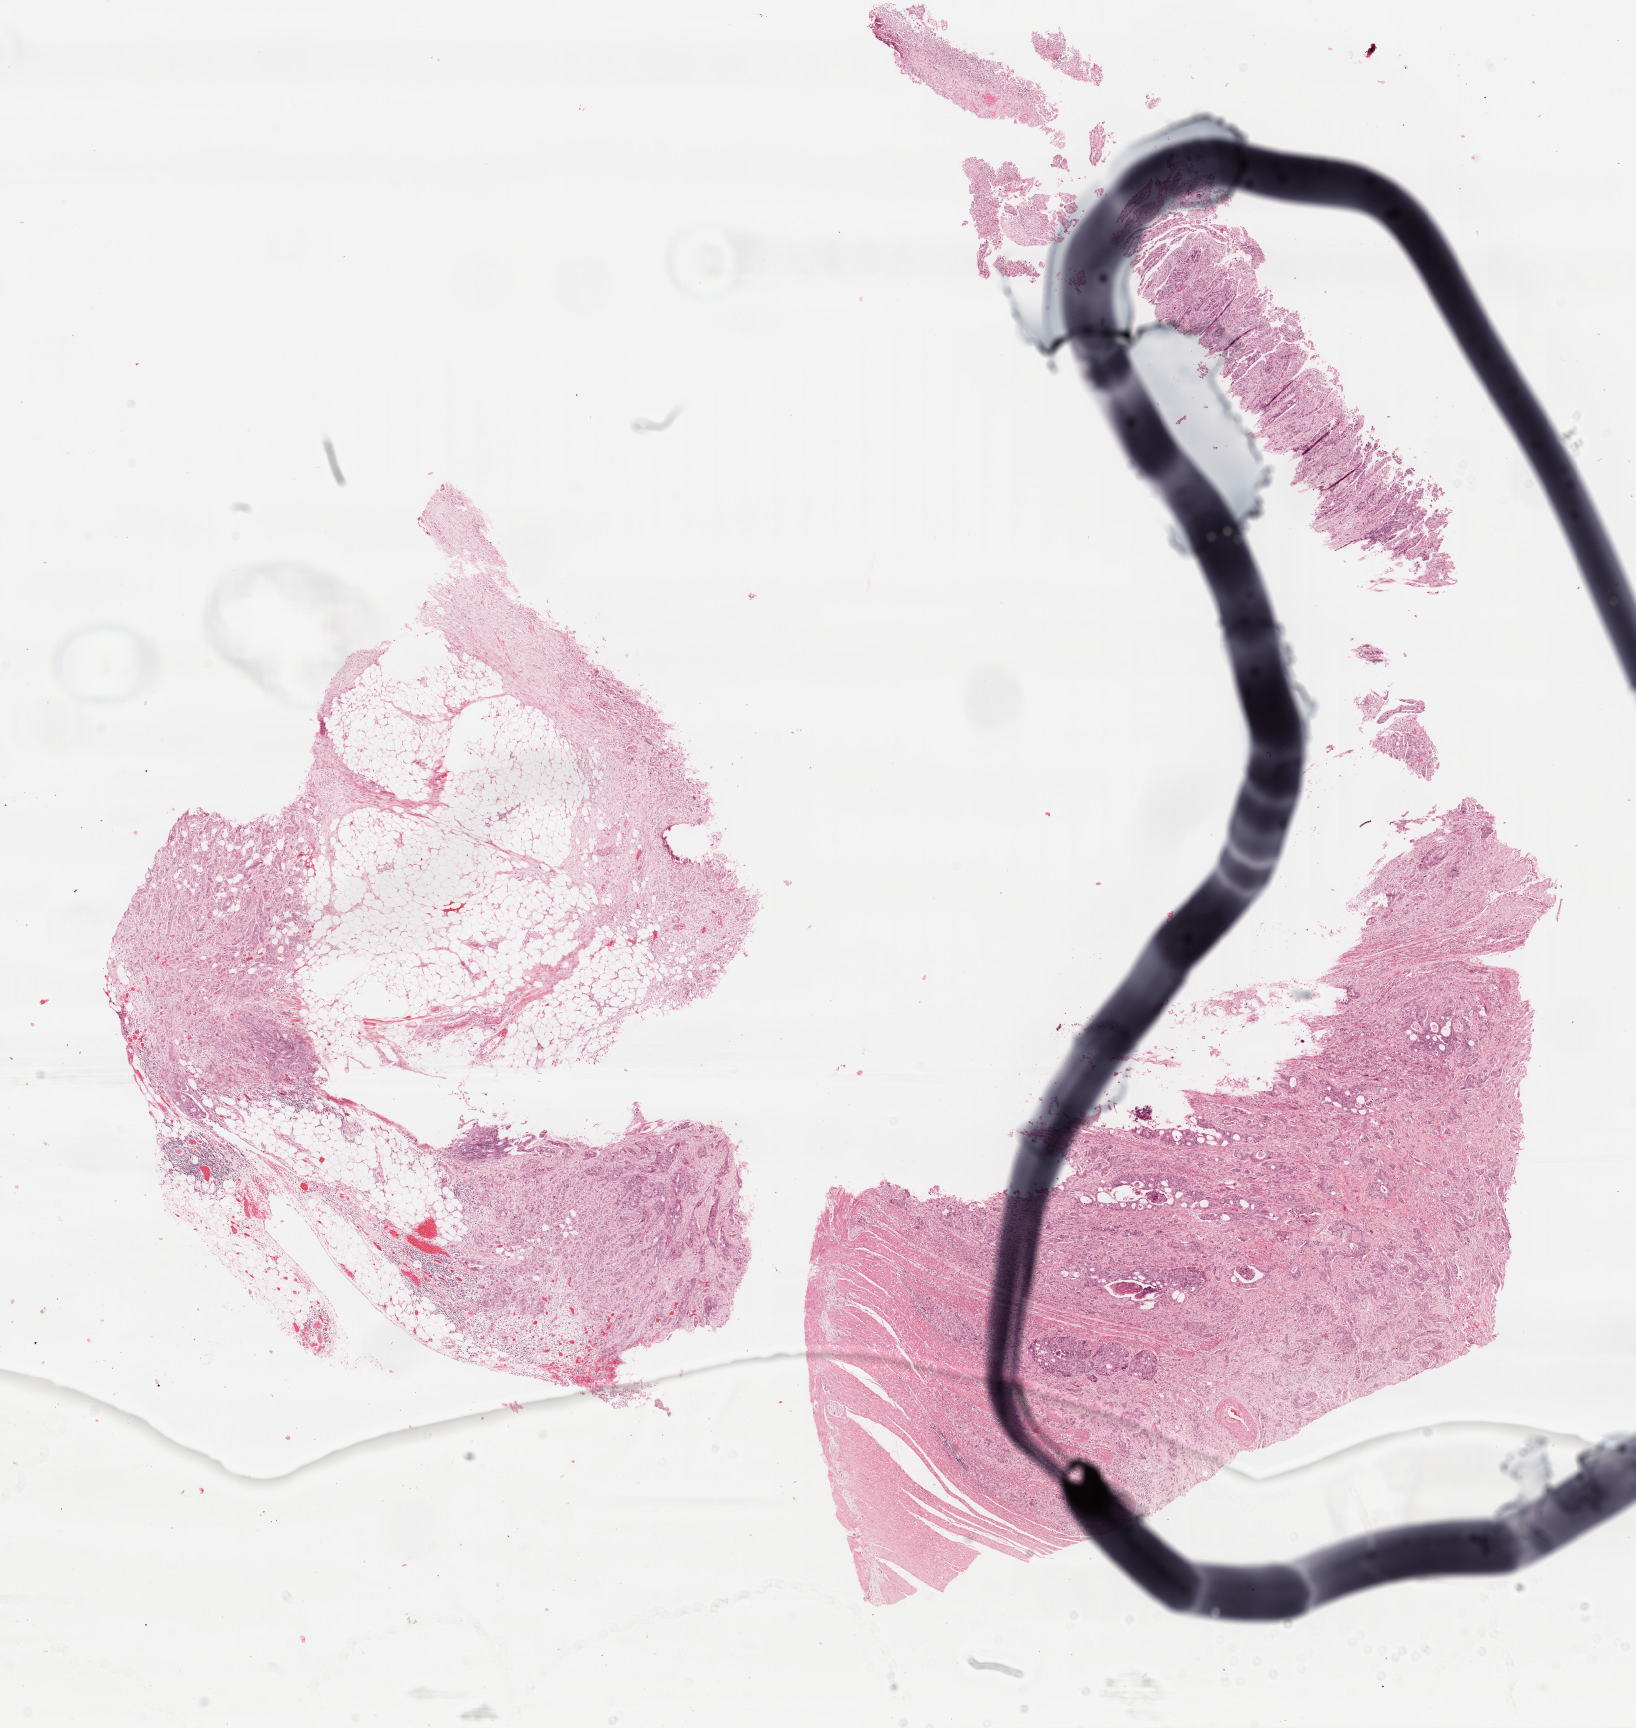
H&E-stained whole-slide image, whole scanned area (about 12.9 x 13.6 mm) shown as a low-resolution overview; FFPE section; primary tumour sample from the colon. Male patient; age at initial diagnosis 65 years.
Lymph nodes positive (case pathology): 0 of 11 examined. Pathologic diagnosis: Adenocarcinoma, NOS (cecum). AJCC pathologic stage: IIA.